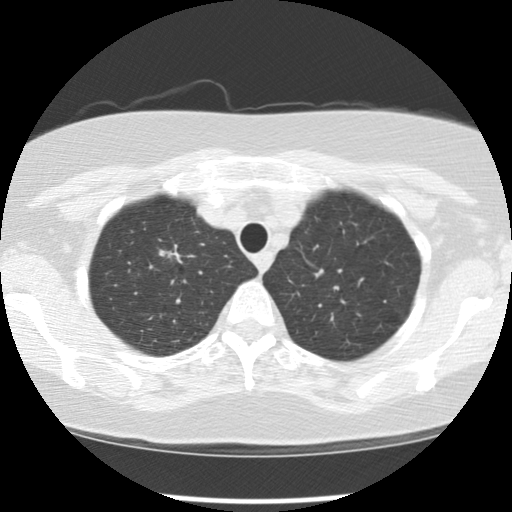
Axial slice from a low-dose chest CT screening exam, baseline annual screen, lung window (W 1500 / L -600 HU), 512 × 512 image matrix, field of view 318 × 318 mm. Female participant, aged 65 years at enrolment. Current smoker at enrolment.
Expert reader's lesion annotation, bounding box (x1, y1, x2, y2) in pixels: (147, 231, 197, 281). The screening reader recorded 2 non-calcified nodules or masses ≥4 mm on this exam (right upper lobe, right upper lobe); which of them this box marks is not recorded. Participant outcome: lung cancer diagnosed 183 days after this screen — large cell carcinoma, NOS, right upper lobe, poorly differentiated (G3), stage IA (AJCC 6th edition), 20 mm at pathology.